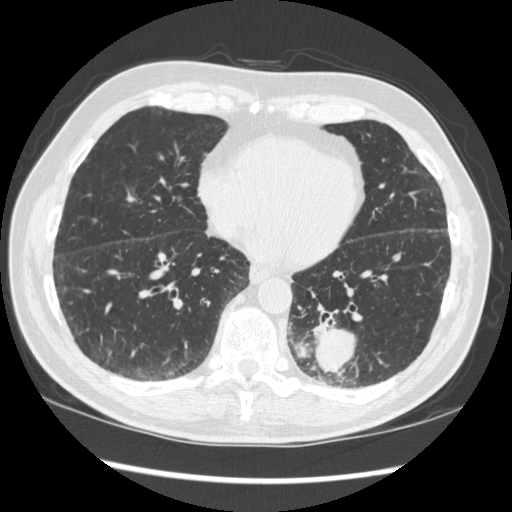
Low-dose screening chest CT, one axial slice. Position 119 of 348 along the scan axis. Reconstruction kernel STANDARD. Lung window (W 1500 / L -600 HU). 1.25 mm slice thickness. 512 × 512 image matrix.
Outlined on this slice (manually delineated by an expert):
- lesion 1 (tumor, lower lobe of left lung): bounding box [x1, y1, x2, y2] px = [298, 328, 356, 375]